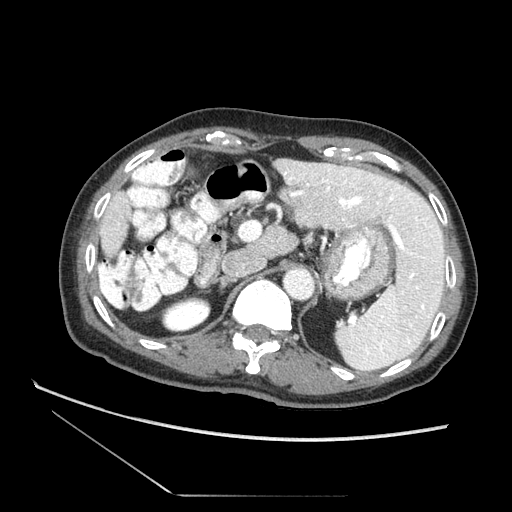
Contrast-enhanced abdominal CT (liver protocol), one axial slice. Position 48 of 73 along the scan axis. Soft-tissue window (W 400 / L 40 HU). 2.5 mm slice thickness. 512 × 512 image matrix, field of view 360 × 360 mm. From the clinical record (not read from this slice): diagnosis: hepatocellular carcinoma (patient treated with transarterial chemoembolisation; whether this scan precedes or follows treatment is not stated here); TNM stage (as recorded): Stage-II; Child-Pugh class: A; tumour differentiation: moderately differentiated; tumour nodularity: multinodular.
Structures marked on this image (semi-automatically segmented with operator editing):
- liver parenchyma outside the tumour (the mass and vessels are separate outlines, so this box may not span the whole liver): bounding box (x1, y1, x2, y2) in pixels: (102, 158, 447, 359)
- liver vessels: (295, 188, 396, 216)